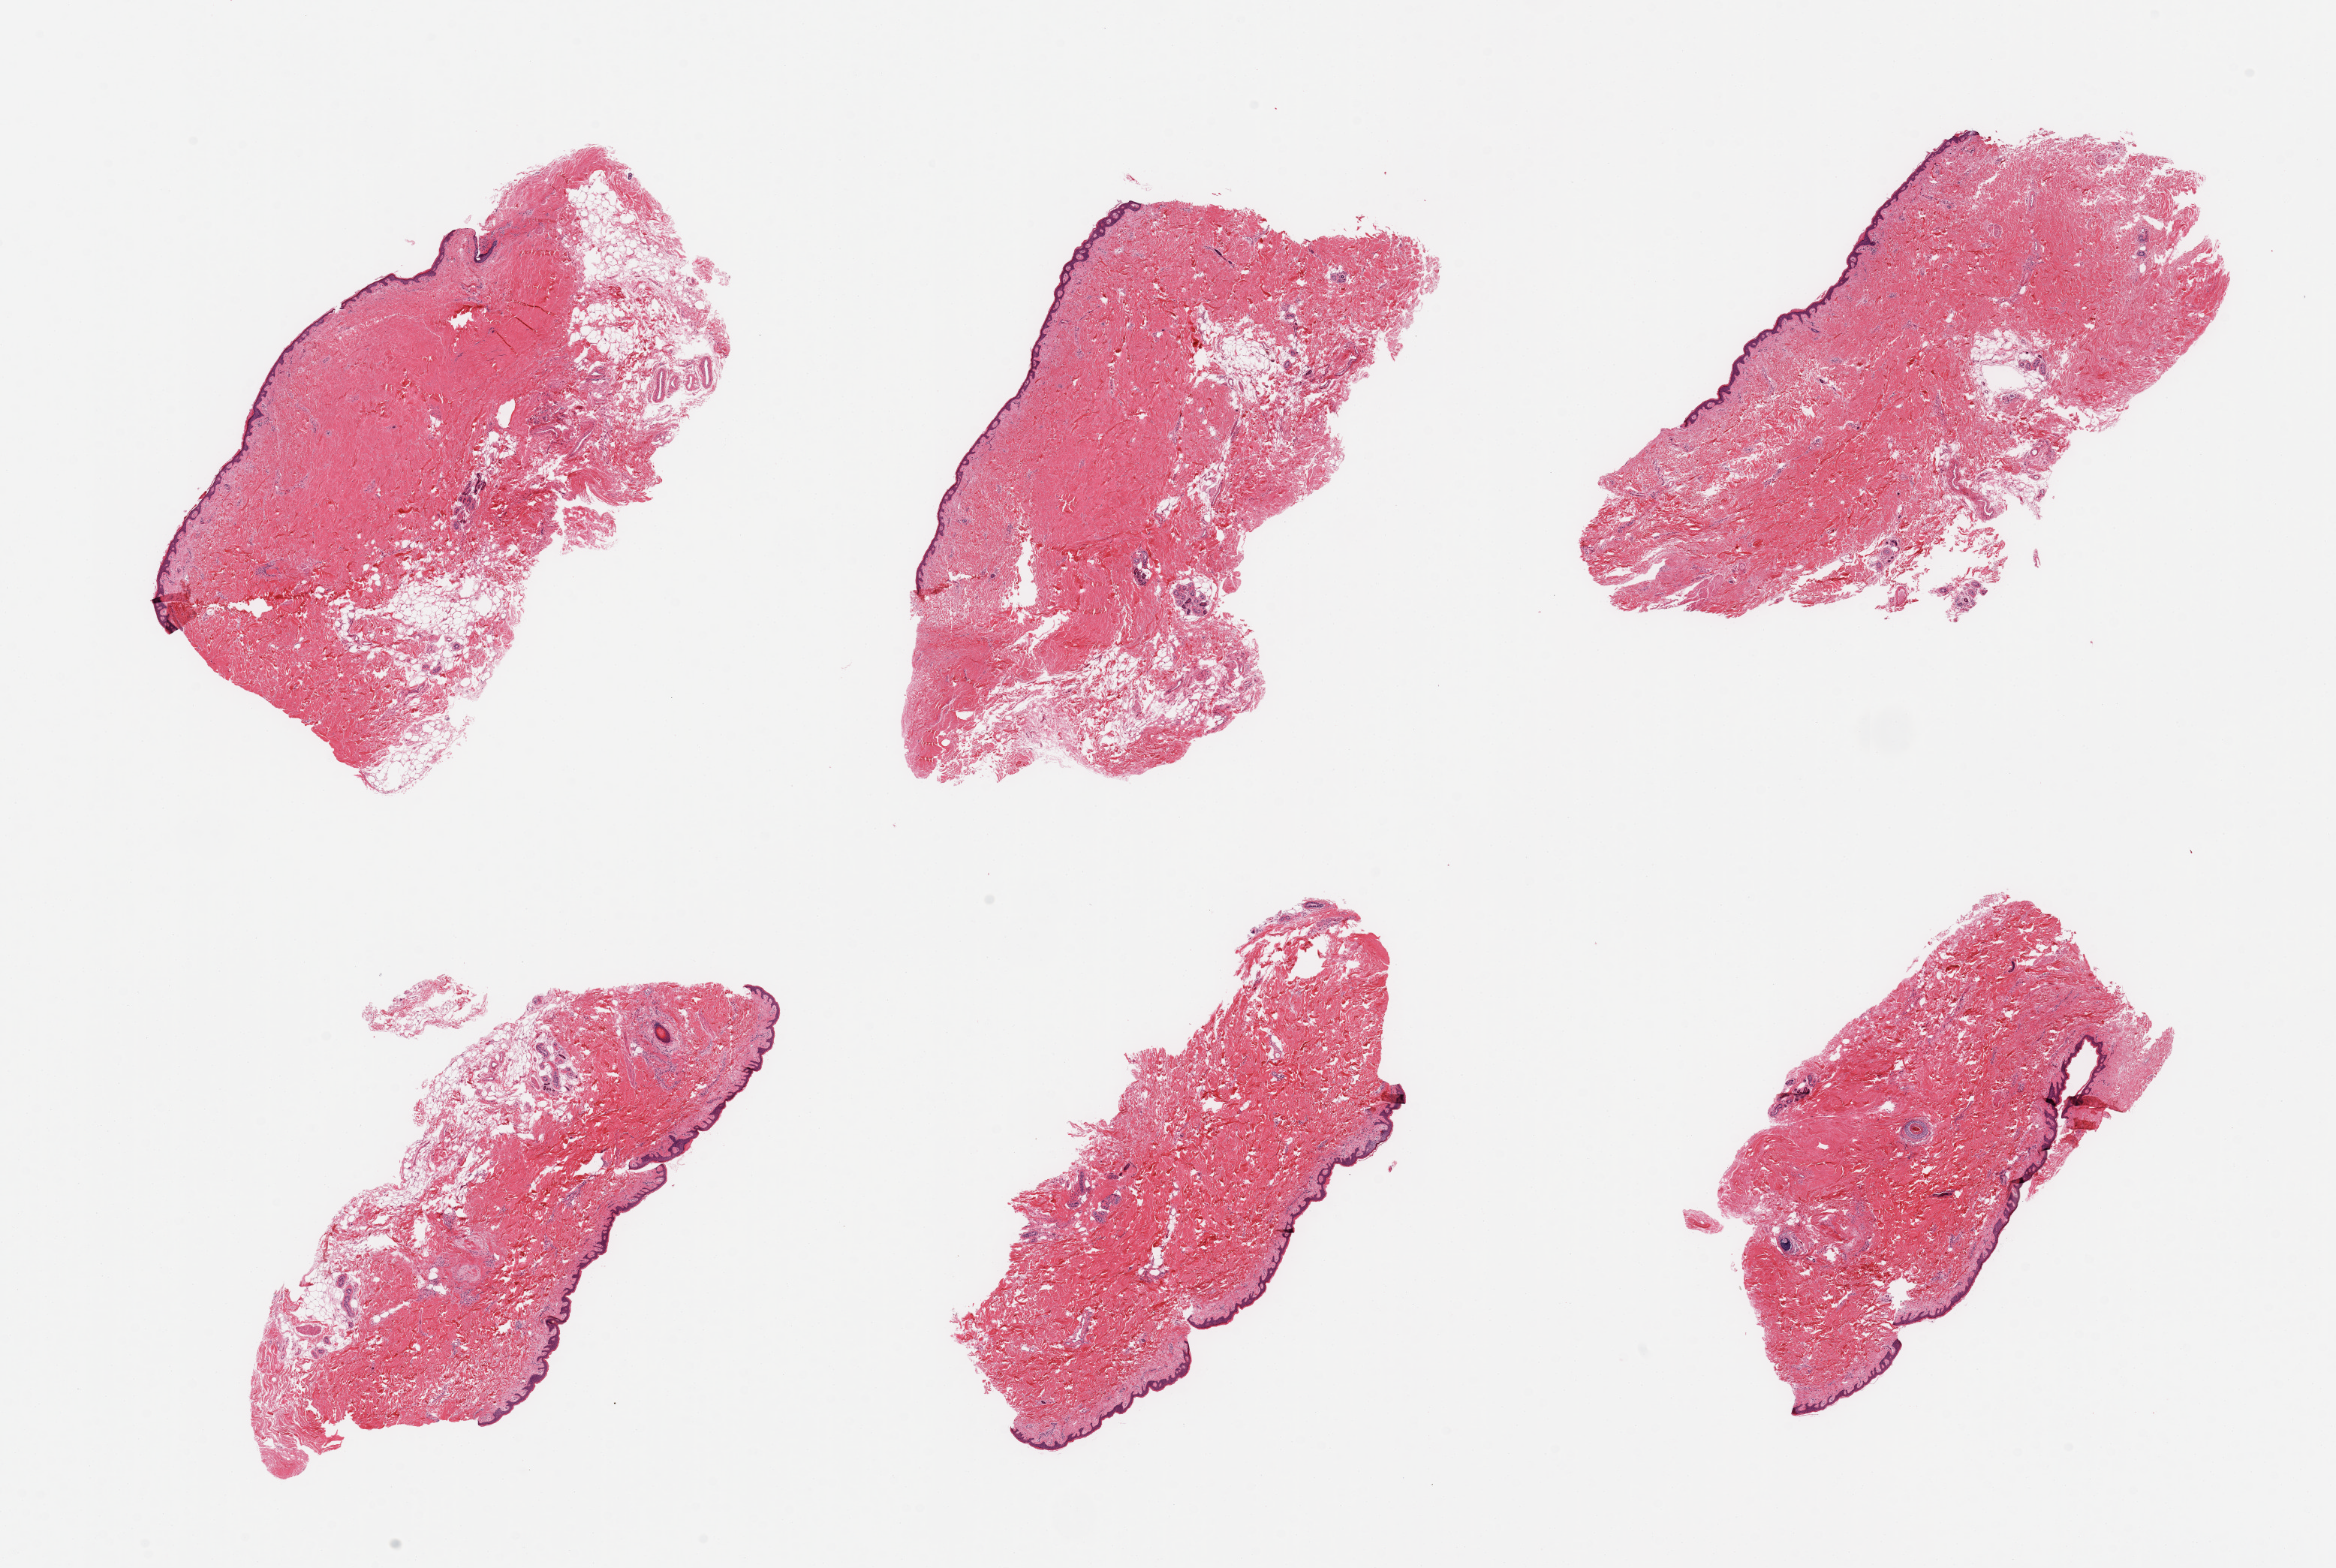
H&E whole-slide image, brightfield, whole scanned area (about 24.6 x 16.5 mm) shown as a low-resolution overview. PAXgene-fixed, paraffin-embedded tissue. Section of skin of suprapubic region (target tissue). Donor tissue sample. Donor: female.
Reviewer comment on this tissue sample: 6 pieces; well trimmed; 20% dermal fat.